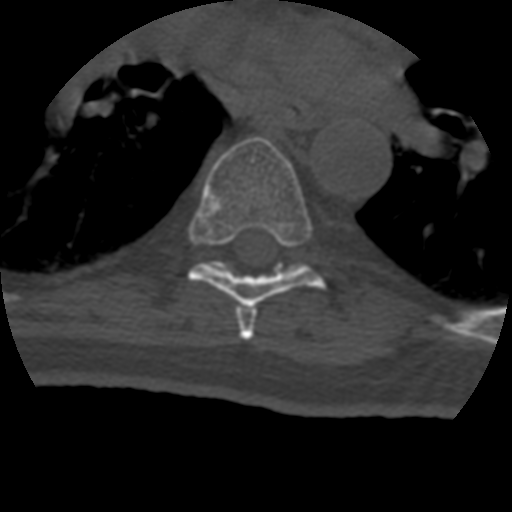
CT including the spine, one axial slice; slice 279 of 399 in the series (ordered by position); 120 kVp; bone window (W 1800 / L 400 HU); 1.25 mm slice thickness; 512 × 512 image matrix. Patient age 69 years. Case-level facts recorded for this patient, not image findings: primary cancer: prostate.
Structures marked on this image (semi-automatic segmentation, software-assisted and operator-edited):
- T6 vertebra: bounding box (x1, y1, x2, y2) in pixels: (235, 306, 256, 340)
- T7 vertebra: (188, 137, 325, 307)
- T8 vertebra: (213, 262, 225, 270)